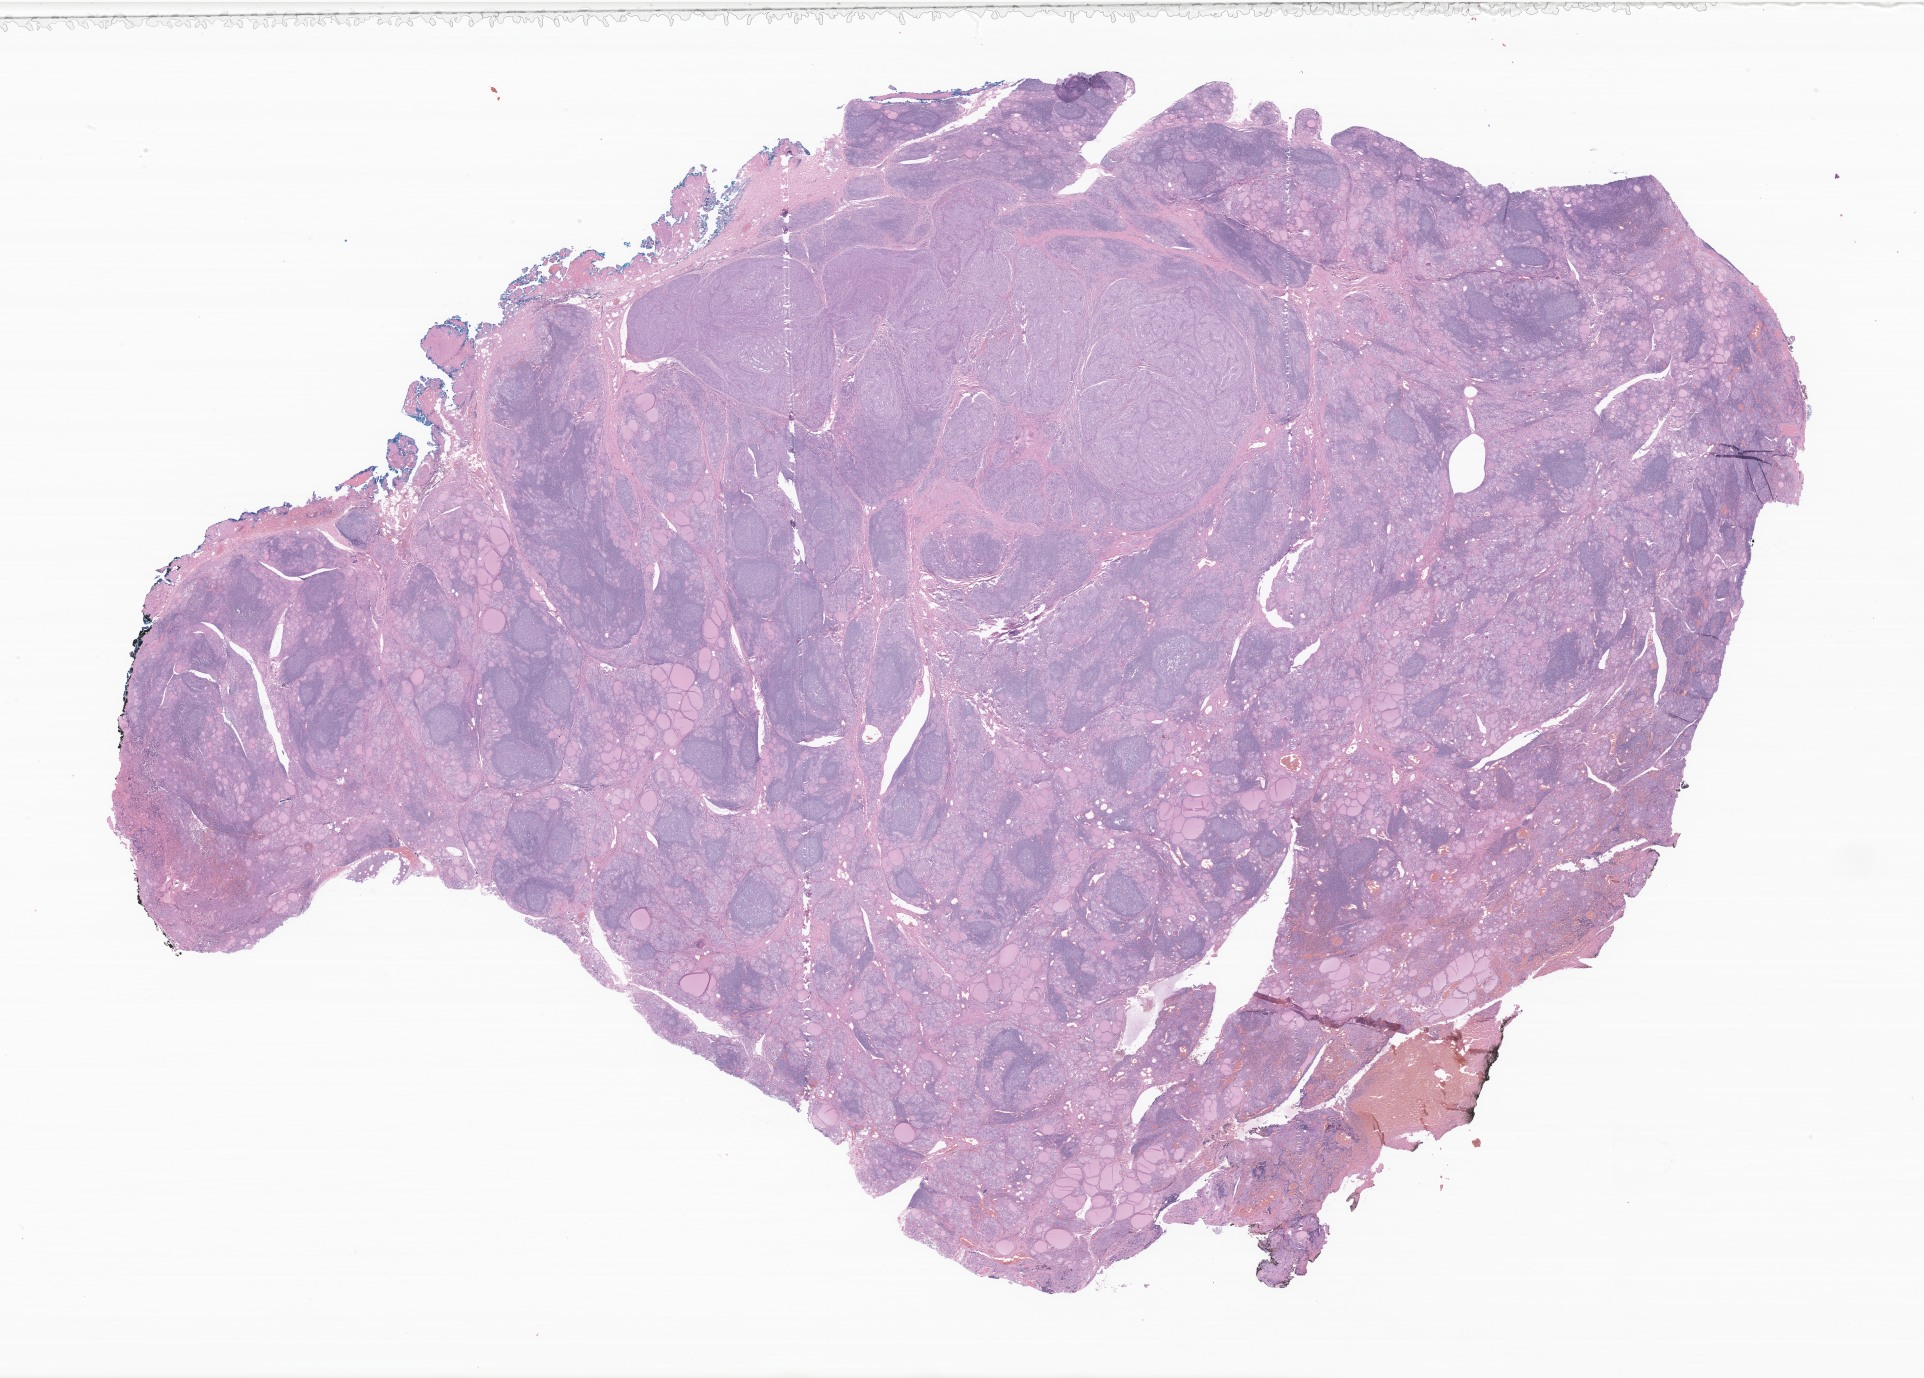
Hematoxylin and eosin (H&E) whole-slide image of tumor tissue from the thyroid — whole scanned area (about 32.4 x 23.2 mm) shown as a low-resolution overview. Formalin-fixed paraffin-embedded section. Patient: female, age 185 months (15 years 5 months).
* recorded diagnosis: Papillary carcinoma, NOS